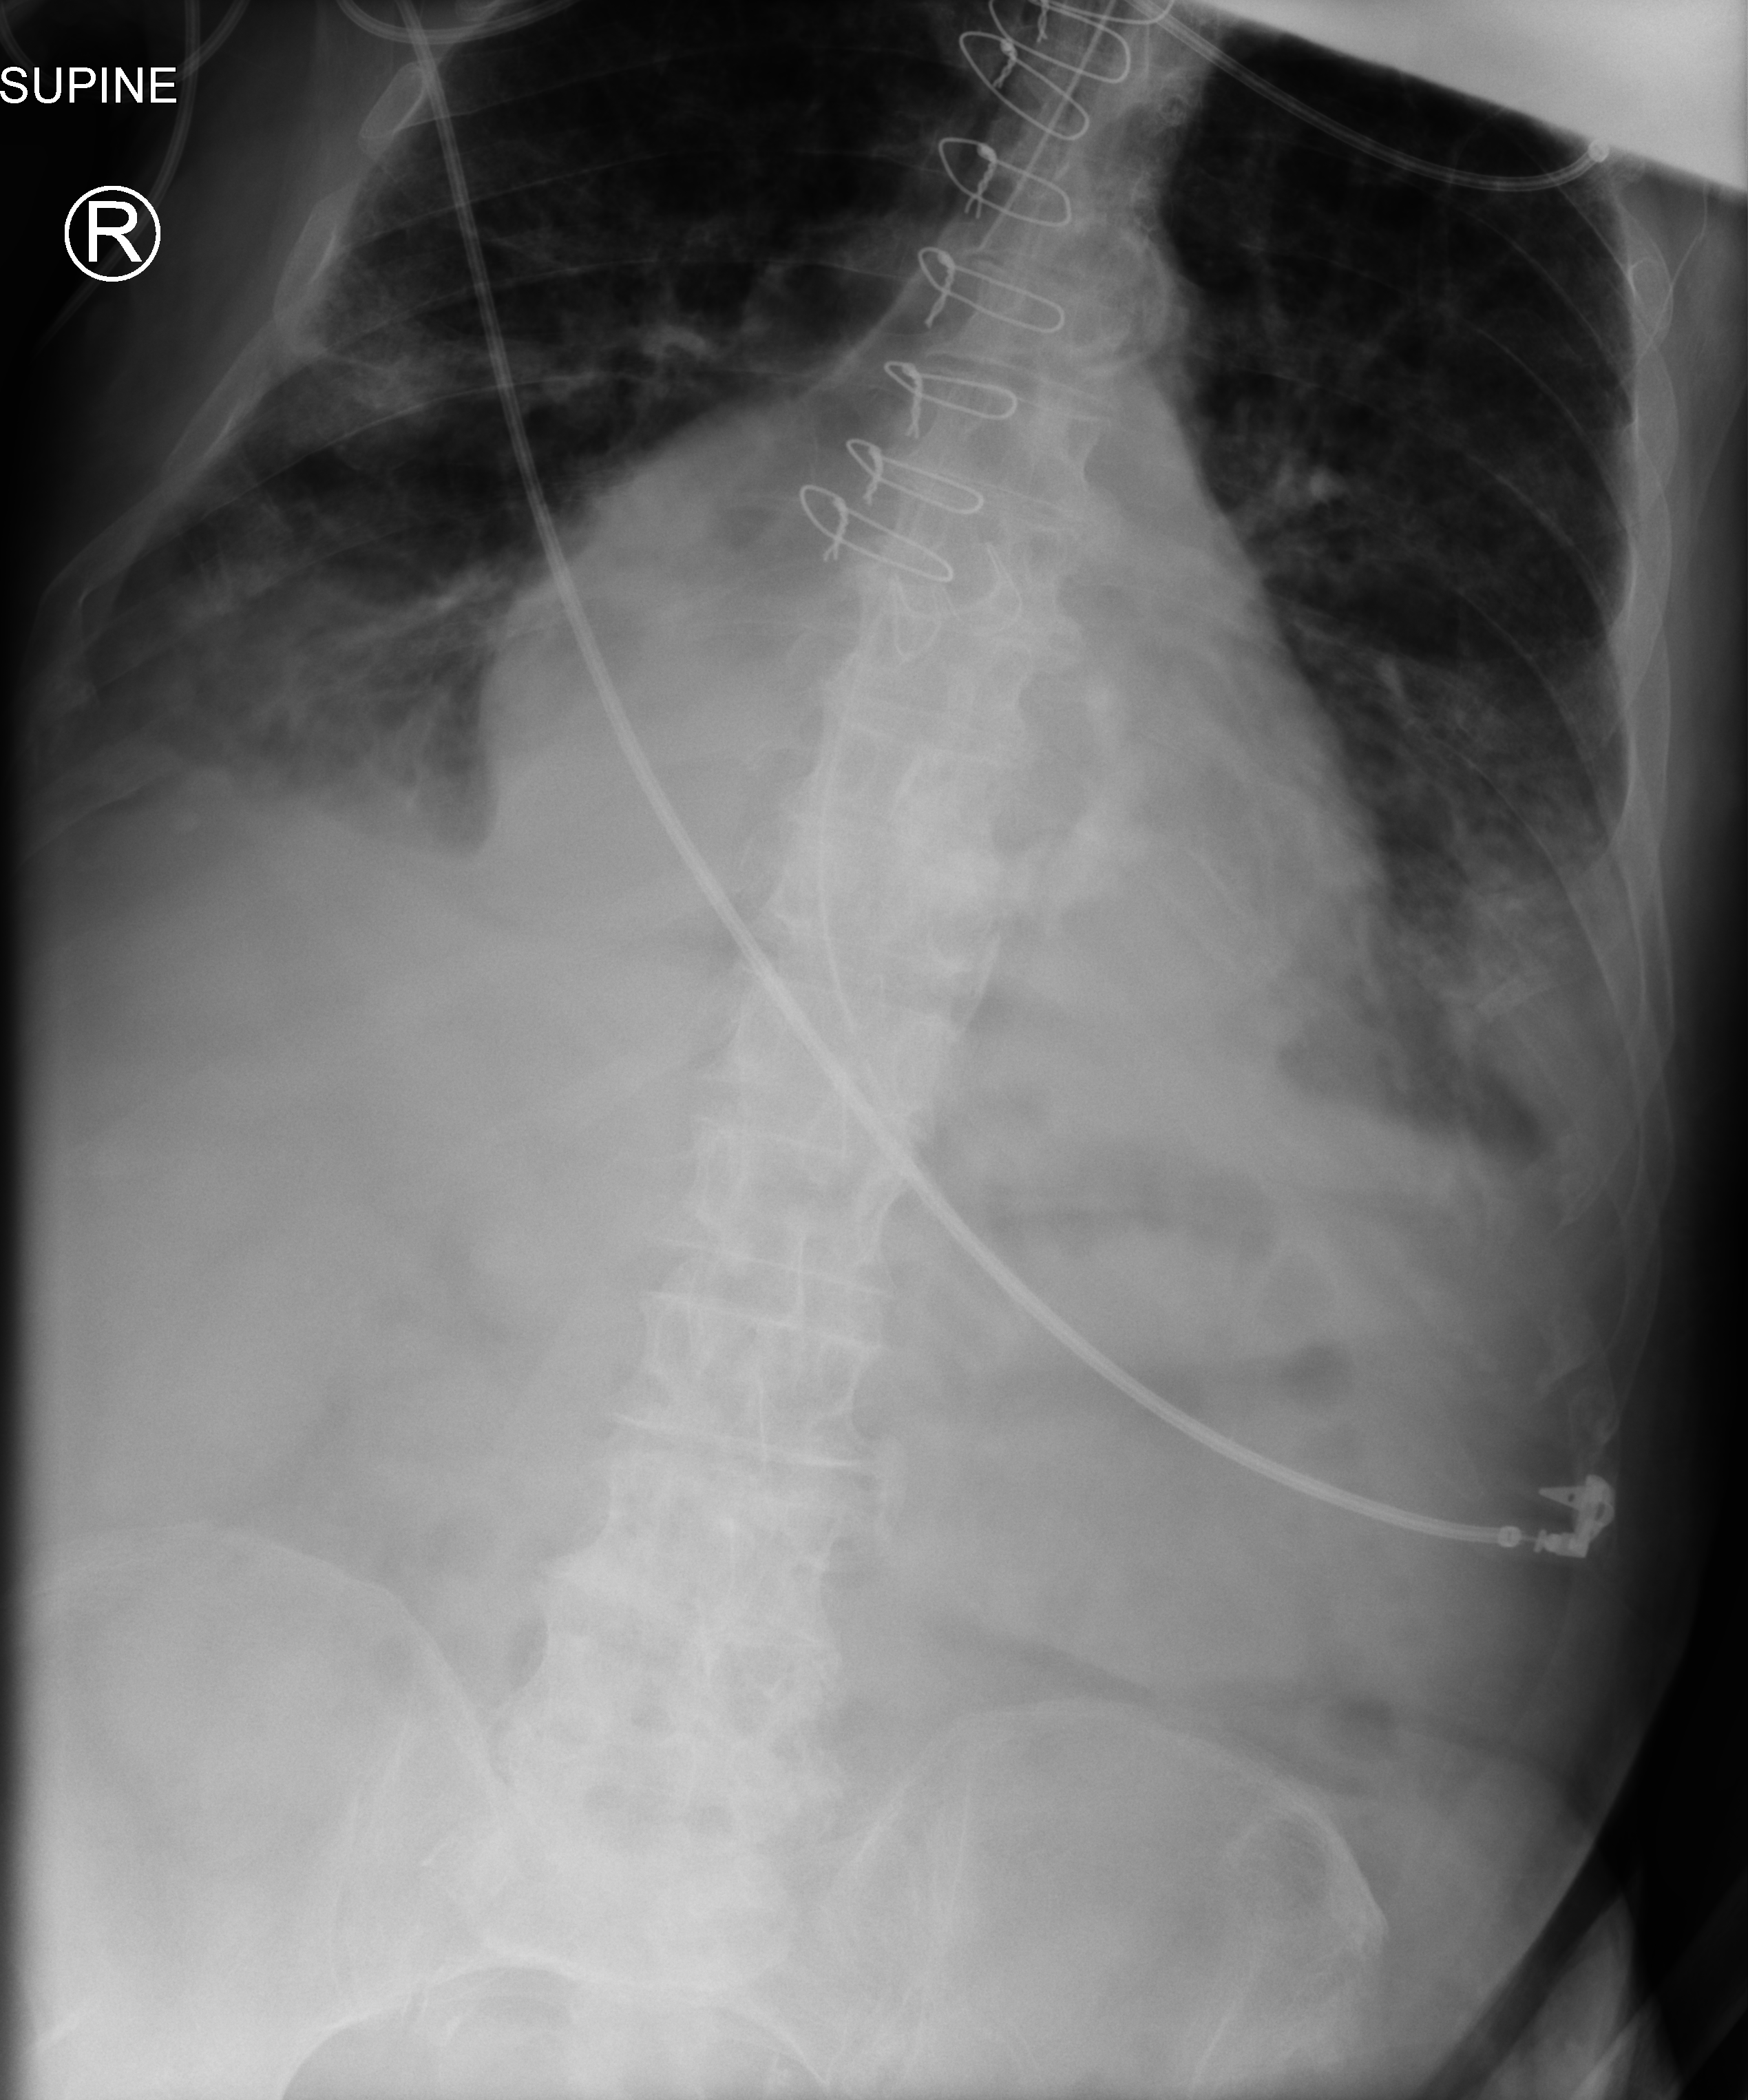
Bedside abdomen radiograph (computed radiography); anteroposterior (AP) projection. Male patient hospitalised with COVID-19, age 75–90 years.
From the hospital-stay record, not from the radiograph (when in the stay this image was taken is not recorded): mechanically ventilated during this hospital stay: yes; length of hospital stay: 40 days.